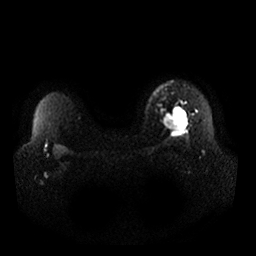
Breast MRI, one axial slice; slice 25 of 32 in the series (ordered by position); diffusion-weighted series; image 2 of 4 stored at this slice position (different b-values; order by instance number); 1.5 T; 4 mm slice thickness; 256 × 256 image matrix, field of view 360 × 360 mm. Female patient.
Annotated regions visible in this slice (manually delineated by an expert):
- tumour on diffusion-weighted imaging: bounding box [x1, y1, x2, y2] px = [169, 107, 188, 133]